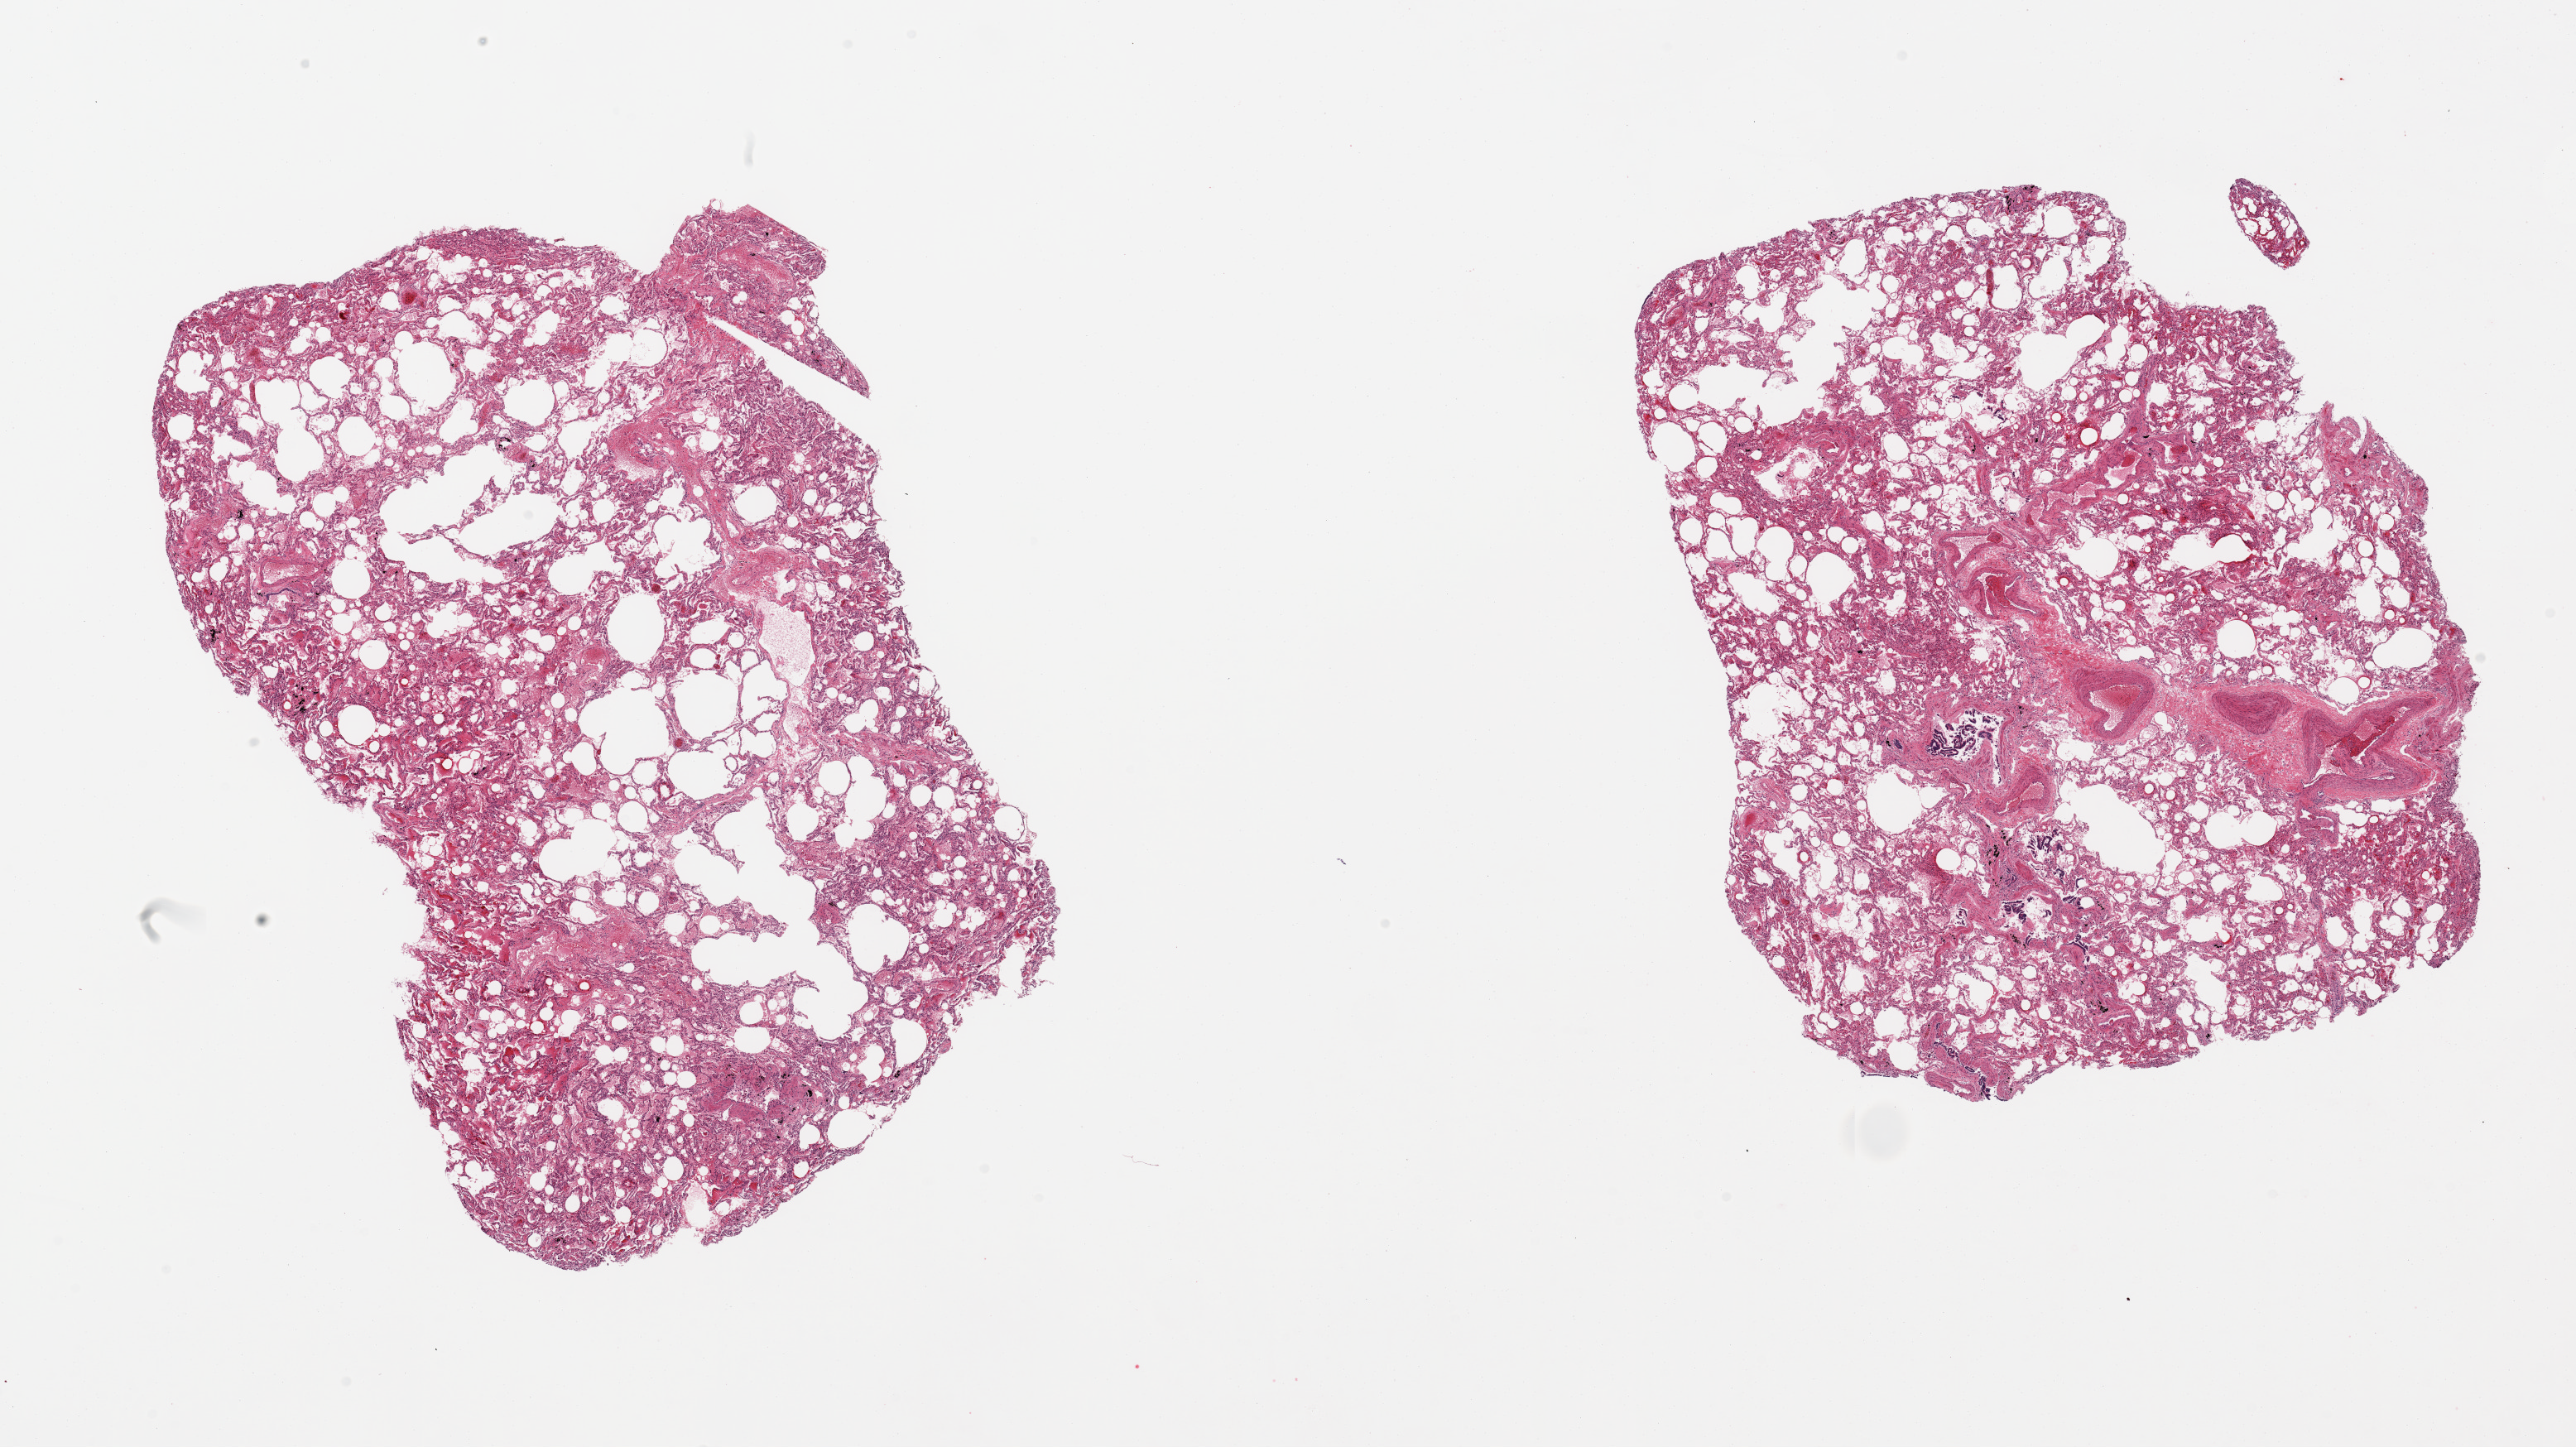
Whole-slide image, hematoxylin and eosin (H&E) stain, brightfield, low-resolution overview of the scanned area, about 24.6 x 13.8 mm; PAXgene-fixed, paraffin-embedded tissue; section of lung (target tissue); tissue donor sample. Donor: male.
Reviewer comment on this tissue sample: 2 pieces, mild- moderate congestion.